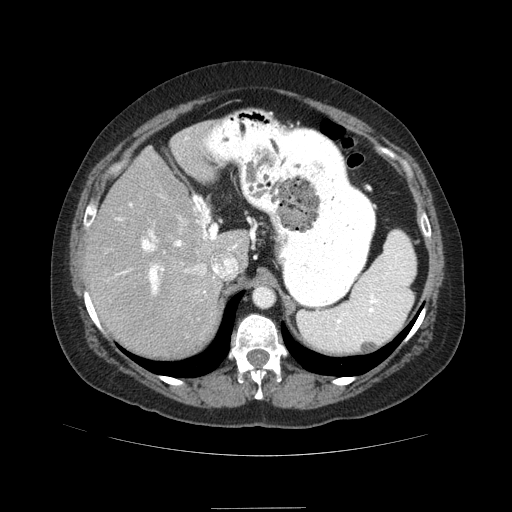
Contrast-enhanced abdominal CT (liver protocol), one axial slice; slice 60 of 89 in the series (ordered by position); soft-tissue window (W 400 / L 40 HU); 2.5 mm slice thickness; 512 × 512 image matrix, field of view 400 × 400 mm. From the clinical record (not read from this slice): diagnosis: hepatocellular carcinoma (patient treated with transarterial chemoembolisation; whether this scan precedes or follows treatment is not stated here); TNM stage (as recorded): Stage-IIIB; Child-Pugh class: A; tumour nodularity: multinodular.
Outlined on this slice (semi-automatically segmented with operator editing):
- abdominal aorta: bounding box (x1, y1, x2, y2) in pixels: (254, 287, 273, 306)
- liver parenchyma outside the tumour (the mass and vessels are separate outlines, so this box may not span the whole liver): (82, 122, 250, 358)
- liver vessels: (91, 137, 237, 295)